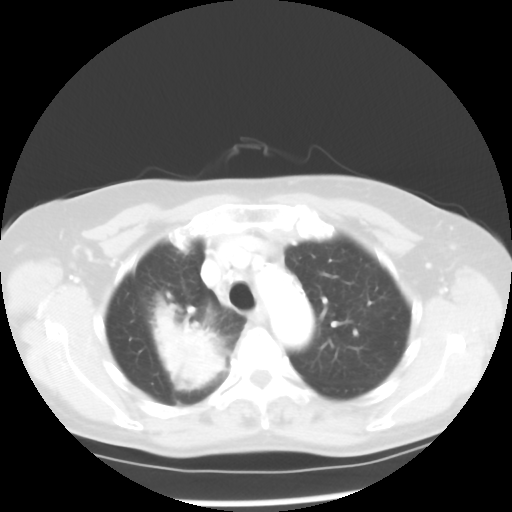
Chest CT, one axial slice. Position 39 of 52 along the scan axis. Reconstruction kernel STANDARD. Lung window (W 1500 / L -600 HU). 5 mm slice thickness. 512 × 512 image matrix, field of view 328 × 328 mm. Female patient, age 60 years. Case-level facts recorded for this patient, not image findings: clinical TNM (as recorded): T2 N1 M1a.
Outlined on this slice (rectangle marked by the reading radiologist):
- lung tumour (recorded histology: adenocarcinoma): bounding box <156,305,228,397> (left, top, right, bottom; pixels)